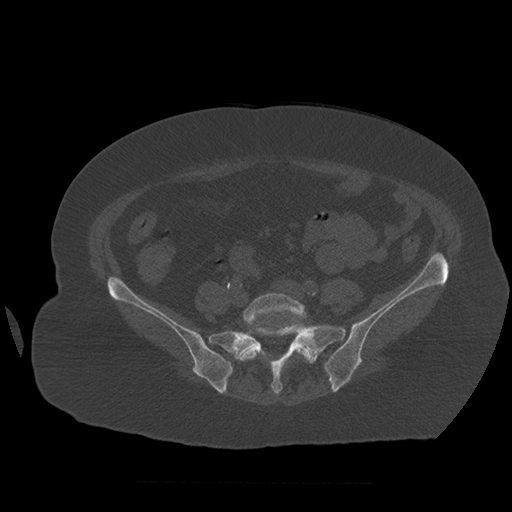
CT including the spine, one axial slice. Position 172 of 399 along the scan axis. 120 kVp. Bone window (W 1800 / L 400 HU). 1.25 mm slice thickness. 512 × 512 image matrix. Patient age 81 years. From the clinical record (not read from this slice): primary cancer: renal.
Outlined on this slice (semi-automatically segmented with operator editing):
- L5 vertebra: bounding box <237,293,314,362> (left, top, right, bottom; pixels)